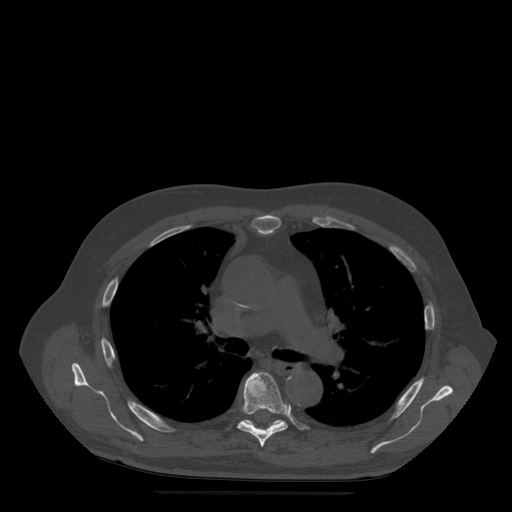
CT including the spine, one axial slice. Position 351 of 522 along the scan axis. Bone window (W 1800 / L 400 HU). 1.25 mm slice thickness. 512 × 512 image matrix, field of view 420 × 420 mm. Patient age 72 years. Case-level facts recorded for this patient, not image findings: primary cancer: prostate.
Structures marked on this image (semi-automatic segmentation, software-assisted and operator-edited):
- T6 vertebra: bounding box (x1, y1, x2, y2) in pixels: (238, 372, 291, 448)
- T7 vertebra: (247, 420, 284, 429)